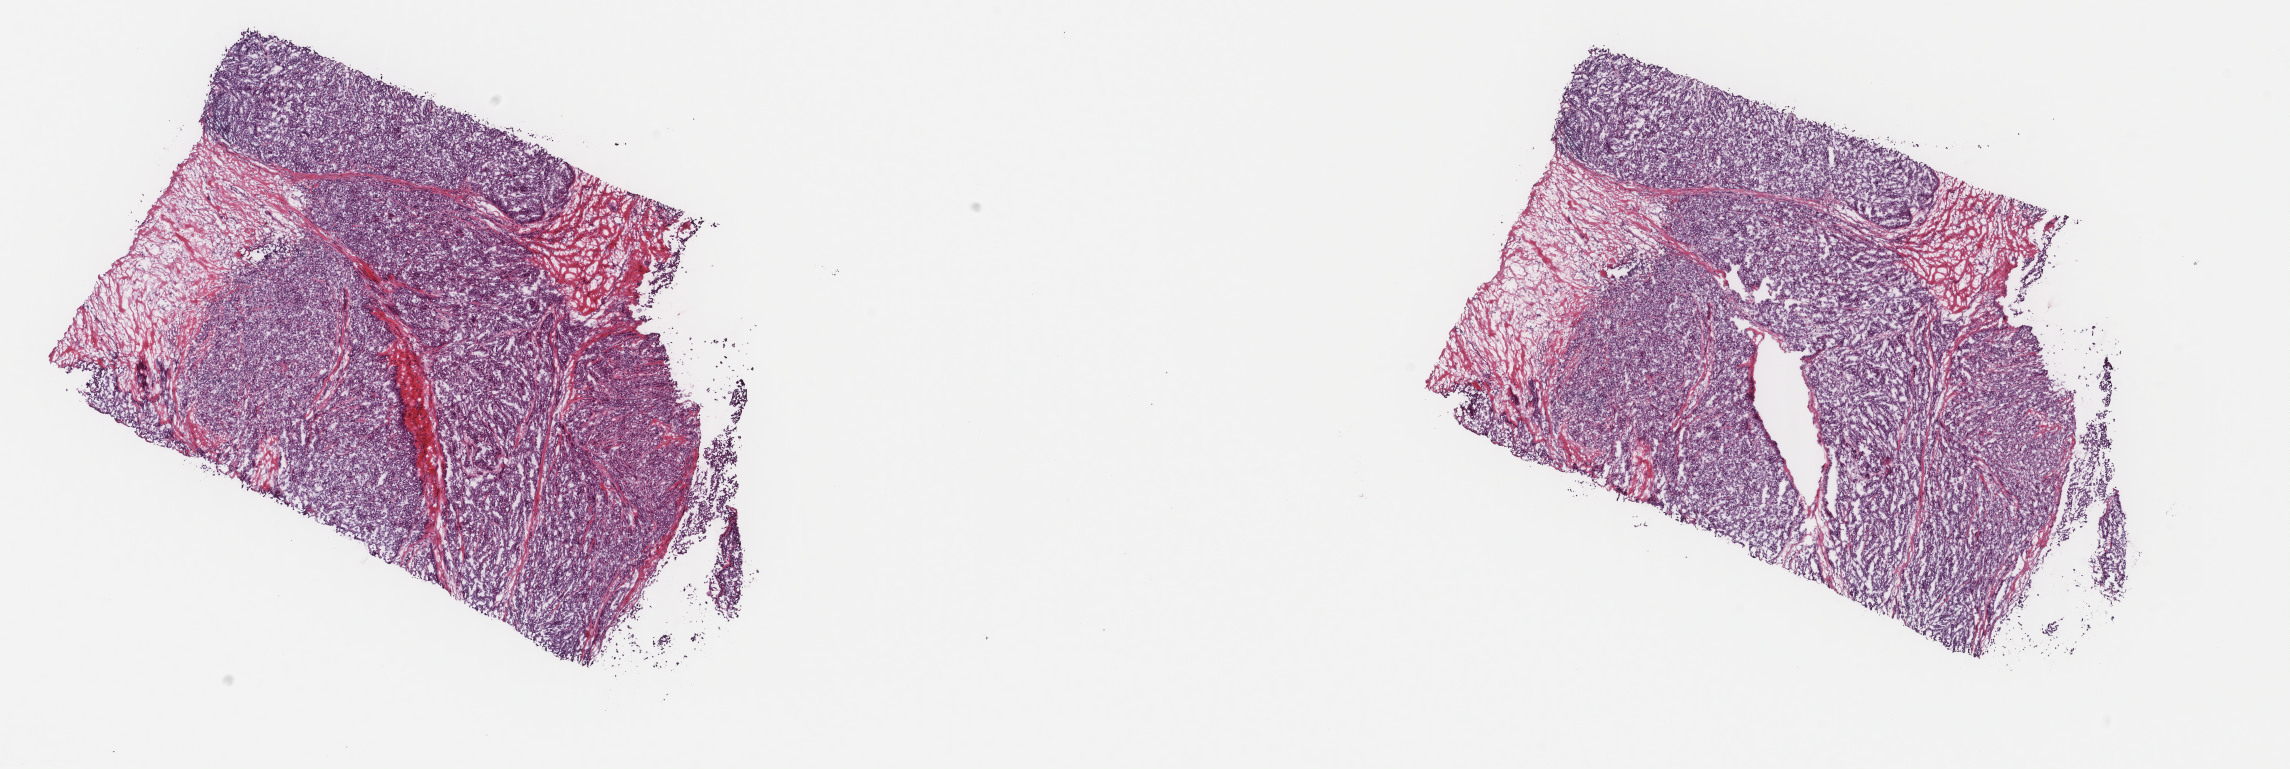
Whole-slide histology image, Hematoxylin and eosin (H&E) stained, low-resolution overview of the scanned area, about 18.2 x 6.1 mm (from a 40x scan). Frozen section from the top of the tissue portion. Metastatic tumour sample, sampled site not recorded. Male, age 79 years at initial diagnosis.
This section: metastatic tumour tissue. Patient diagnosis: Malignant melanoma, NOS.